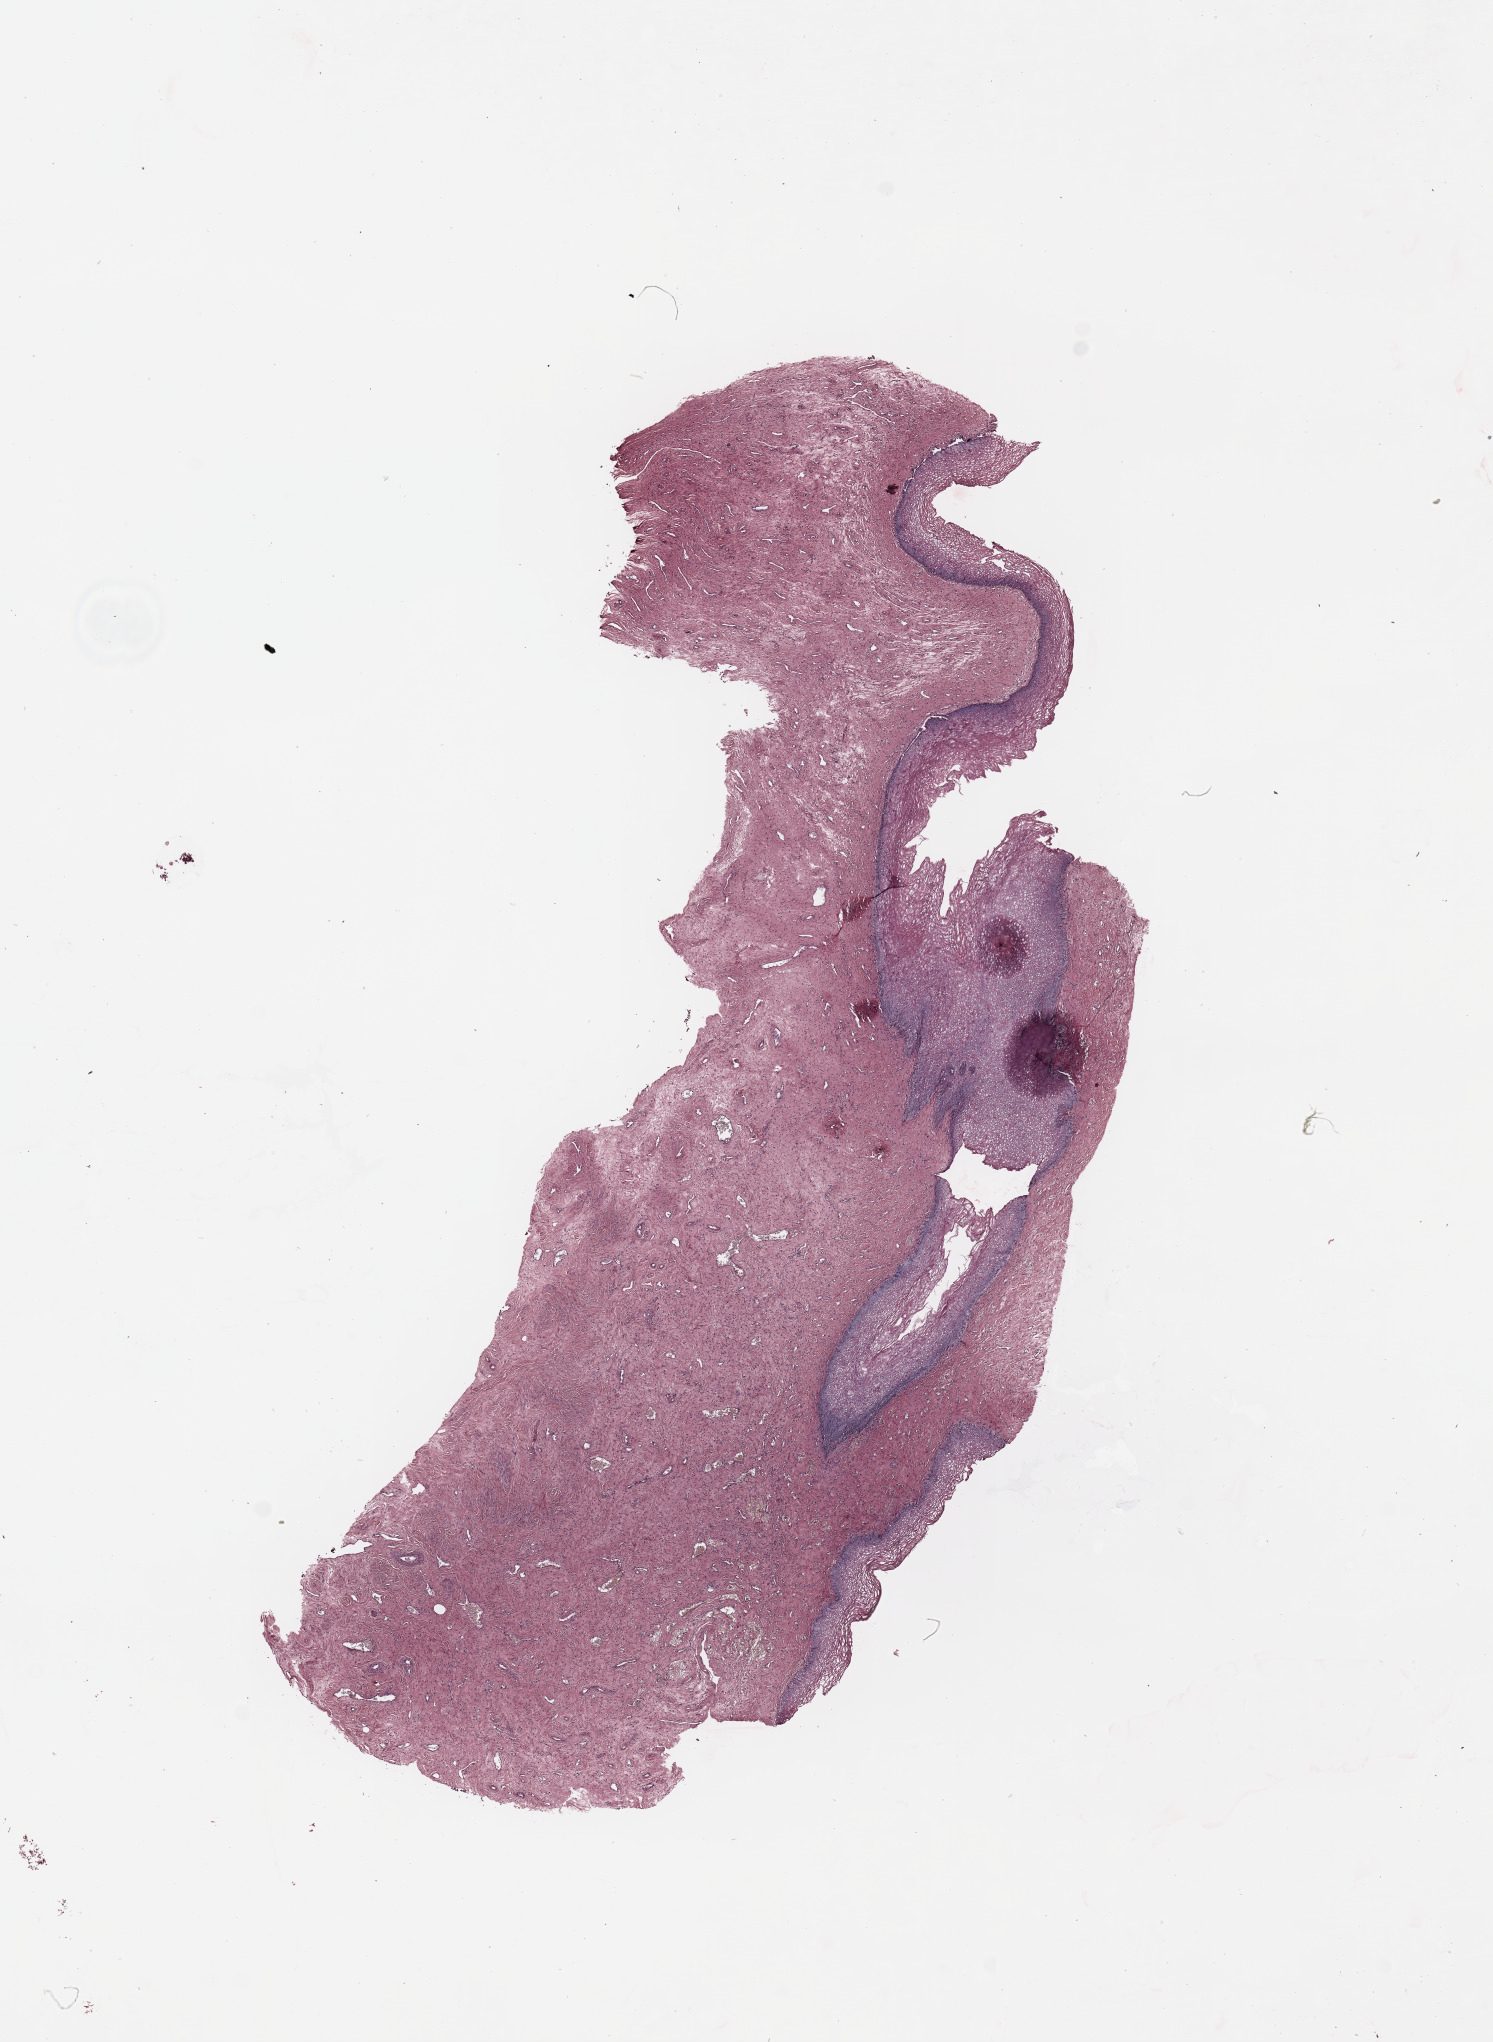
H&E-stained whole-slide image, a low-resolution overview of the entire scanned area, about 11.8 x 16.2 mm; normal (non-tumour) tissue sample, uterus. Patient: female, age 75 years.
This section: normal (non-tumour) tissue from the same patient. Patient diagnosis: Endometrioid adenocarcinoma, NOS.